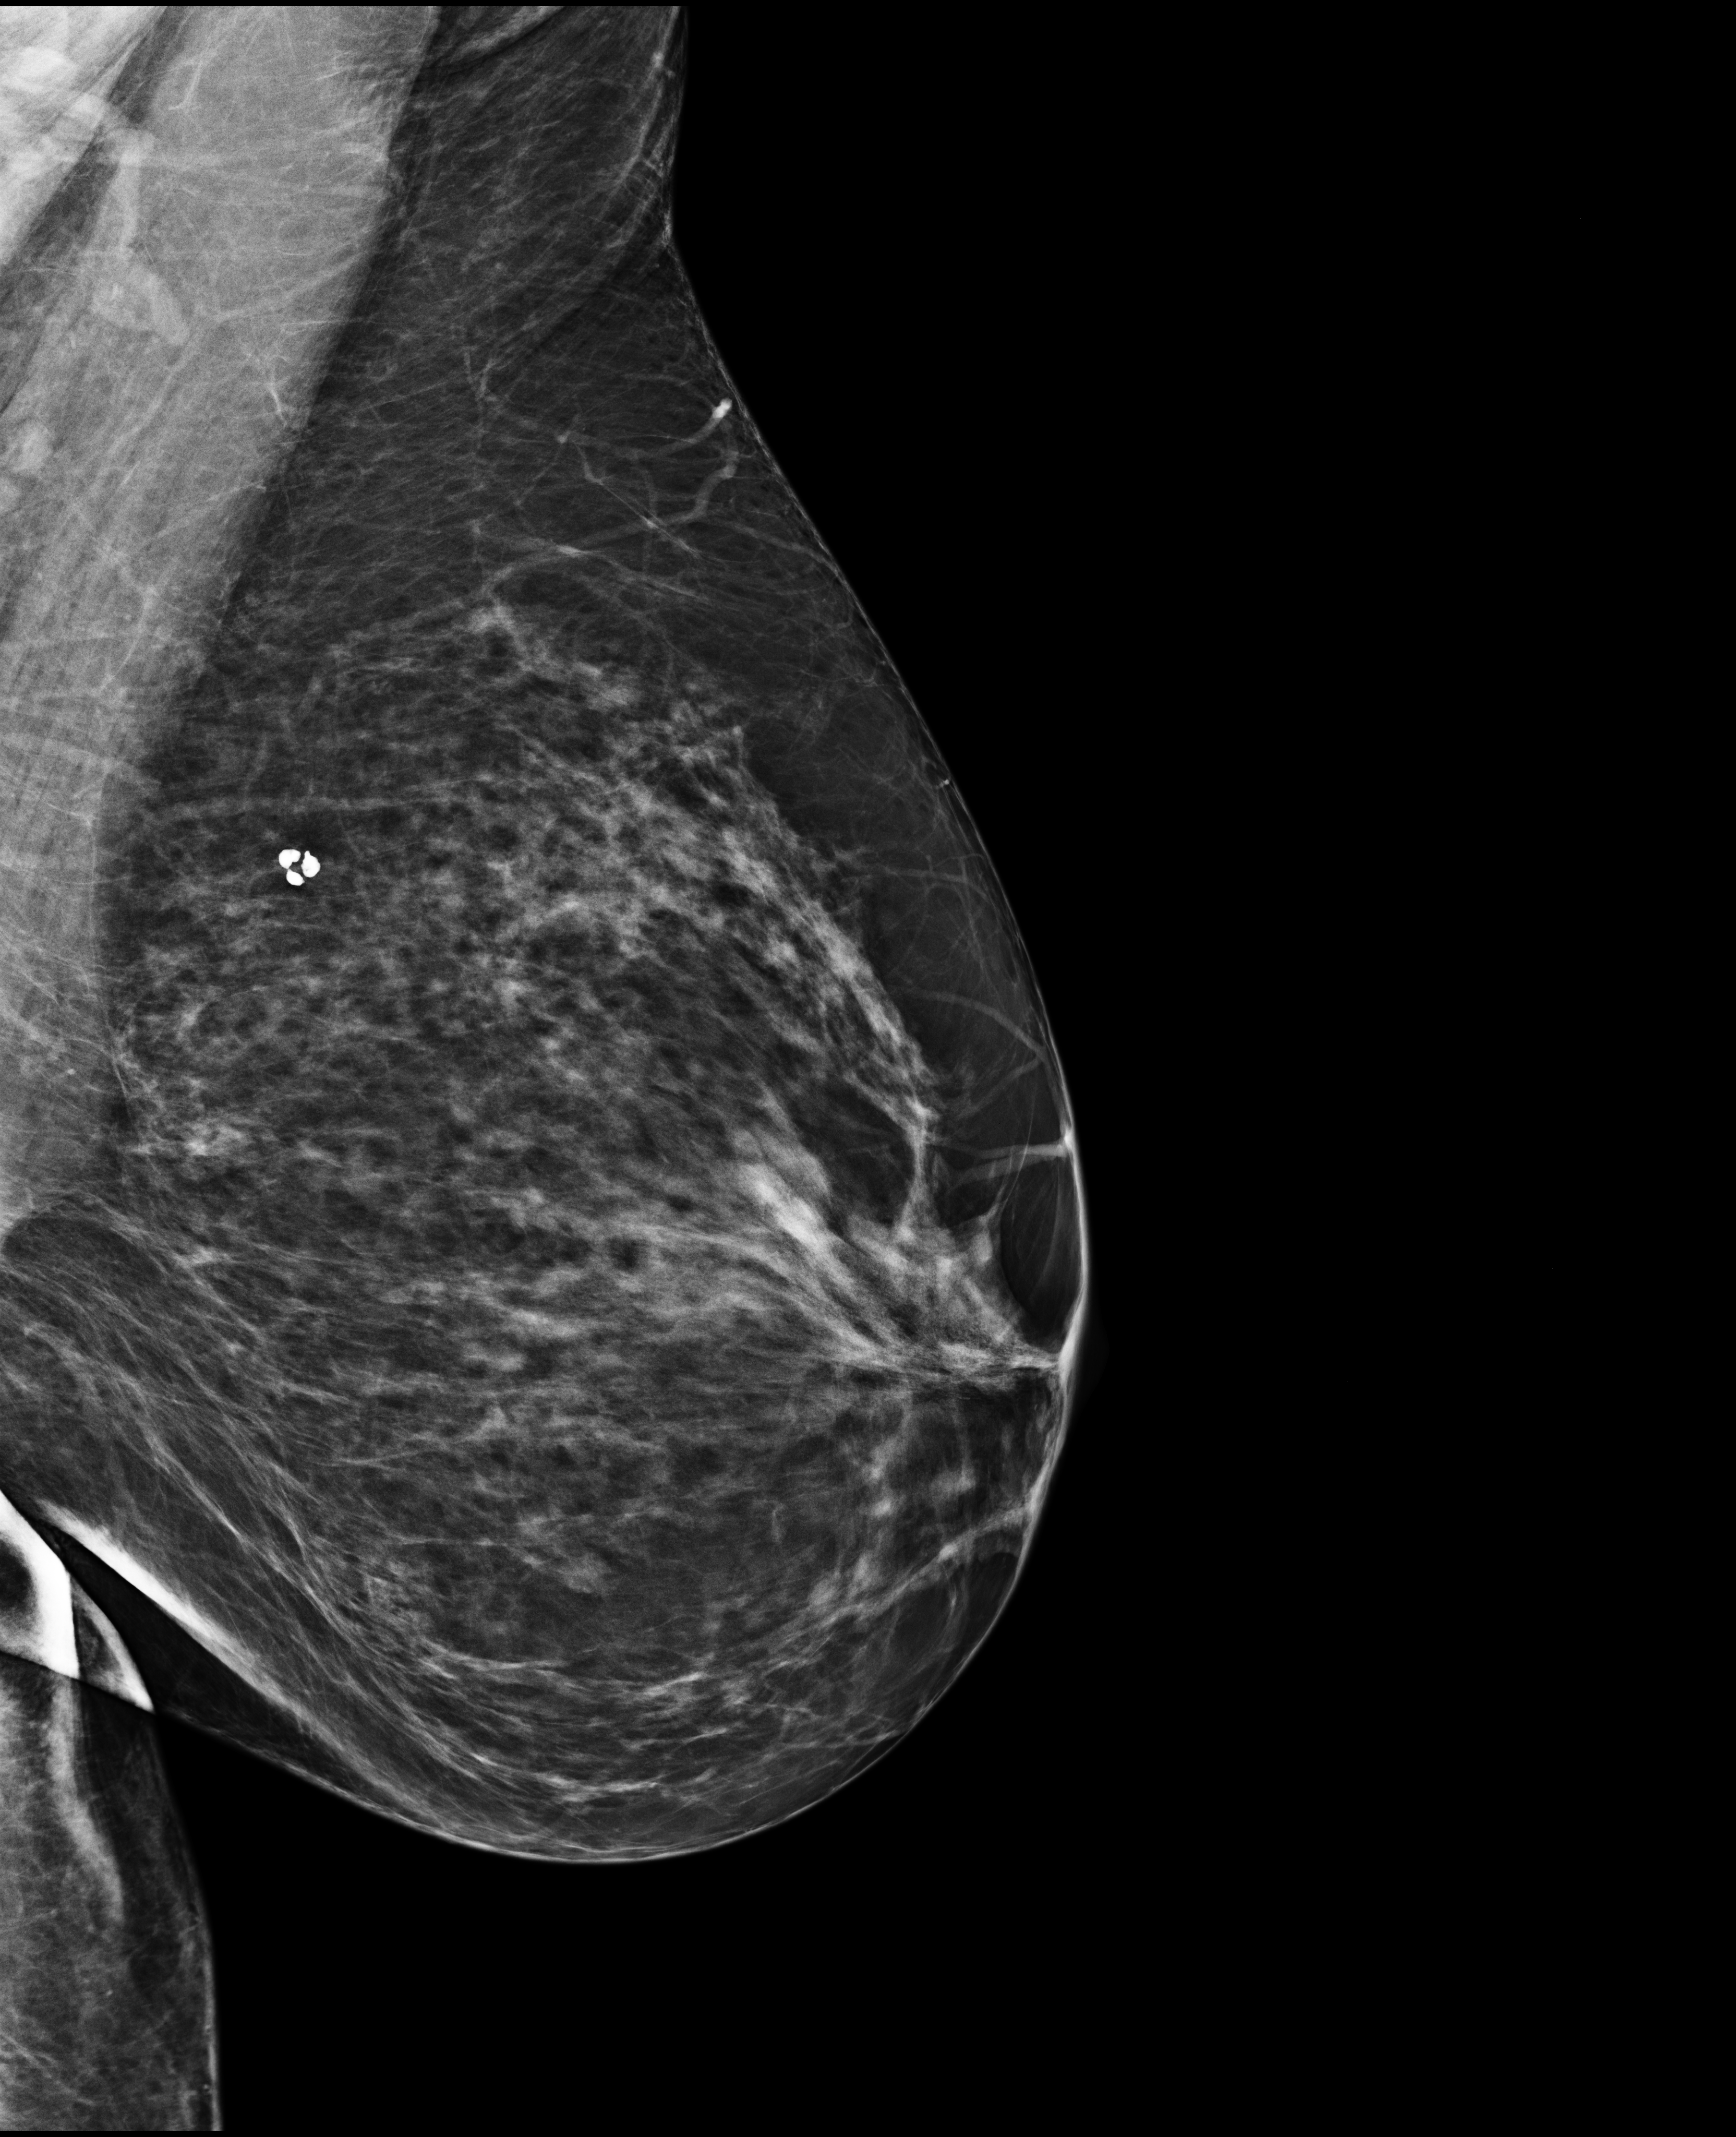
Annual screening mammography examination.
Image type: full-field digital mammogram. Breast: left. Projection: MLO view.